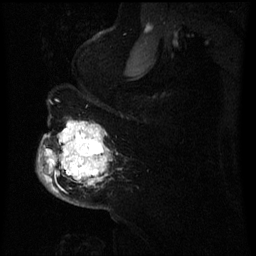
Breast MRI (dynamic contrast-enhanced), one sagittal slice; position 46 of 60 along the scan axis; dynamic contrast-enhanced series, image 2 of 3 at this slice position (ordered by acquisition); 1.5 T; TE 4.2 ms, TR 8 ms; 2.5 mm slice thickness; 256 × 256 image matrix. Female patient, age 50 years.
Structures marked on this image (semi-automatically segmented with operator editing):
- analysis volume of interest (the breast-tissue region the enhancement analysis was run in; not a lesion): bounding box <41,122,108,191> (left, top, right, bottom; pixels)
- tumour enhancement mask (voxels above the 70 % enhancement threshold inside the analysis volume of interest): <46,126,106,181>